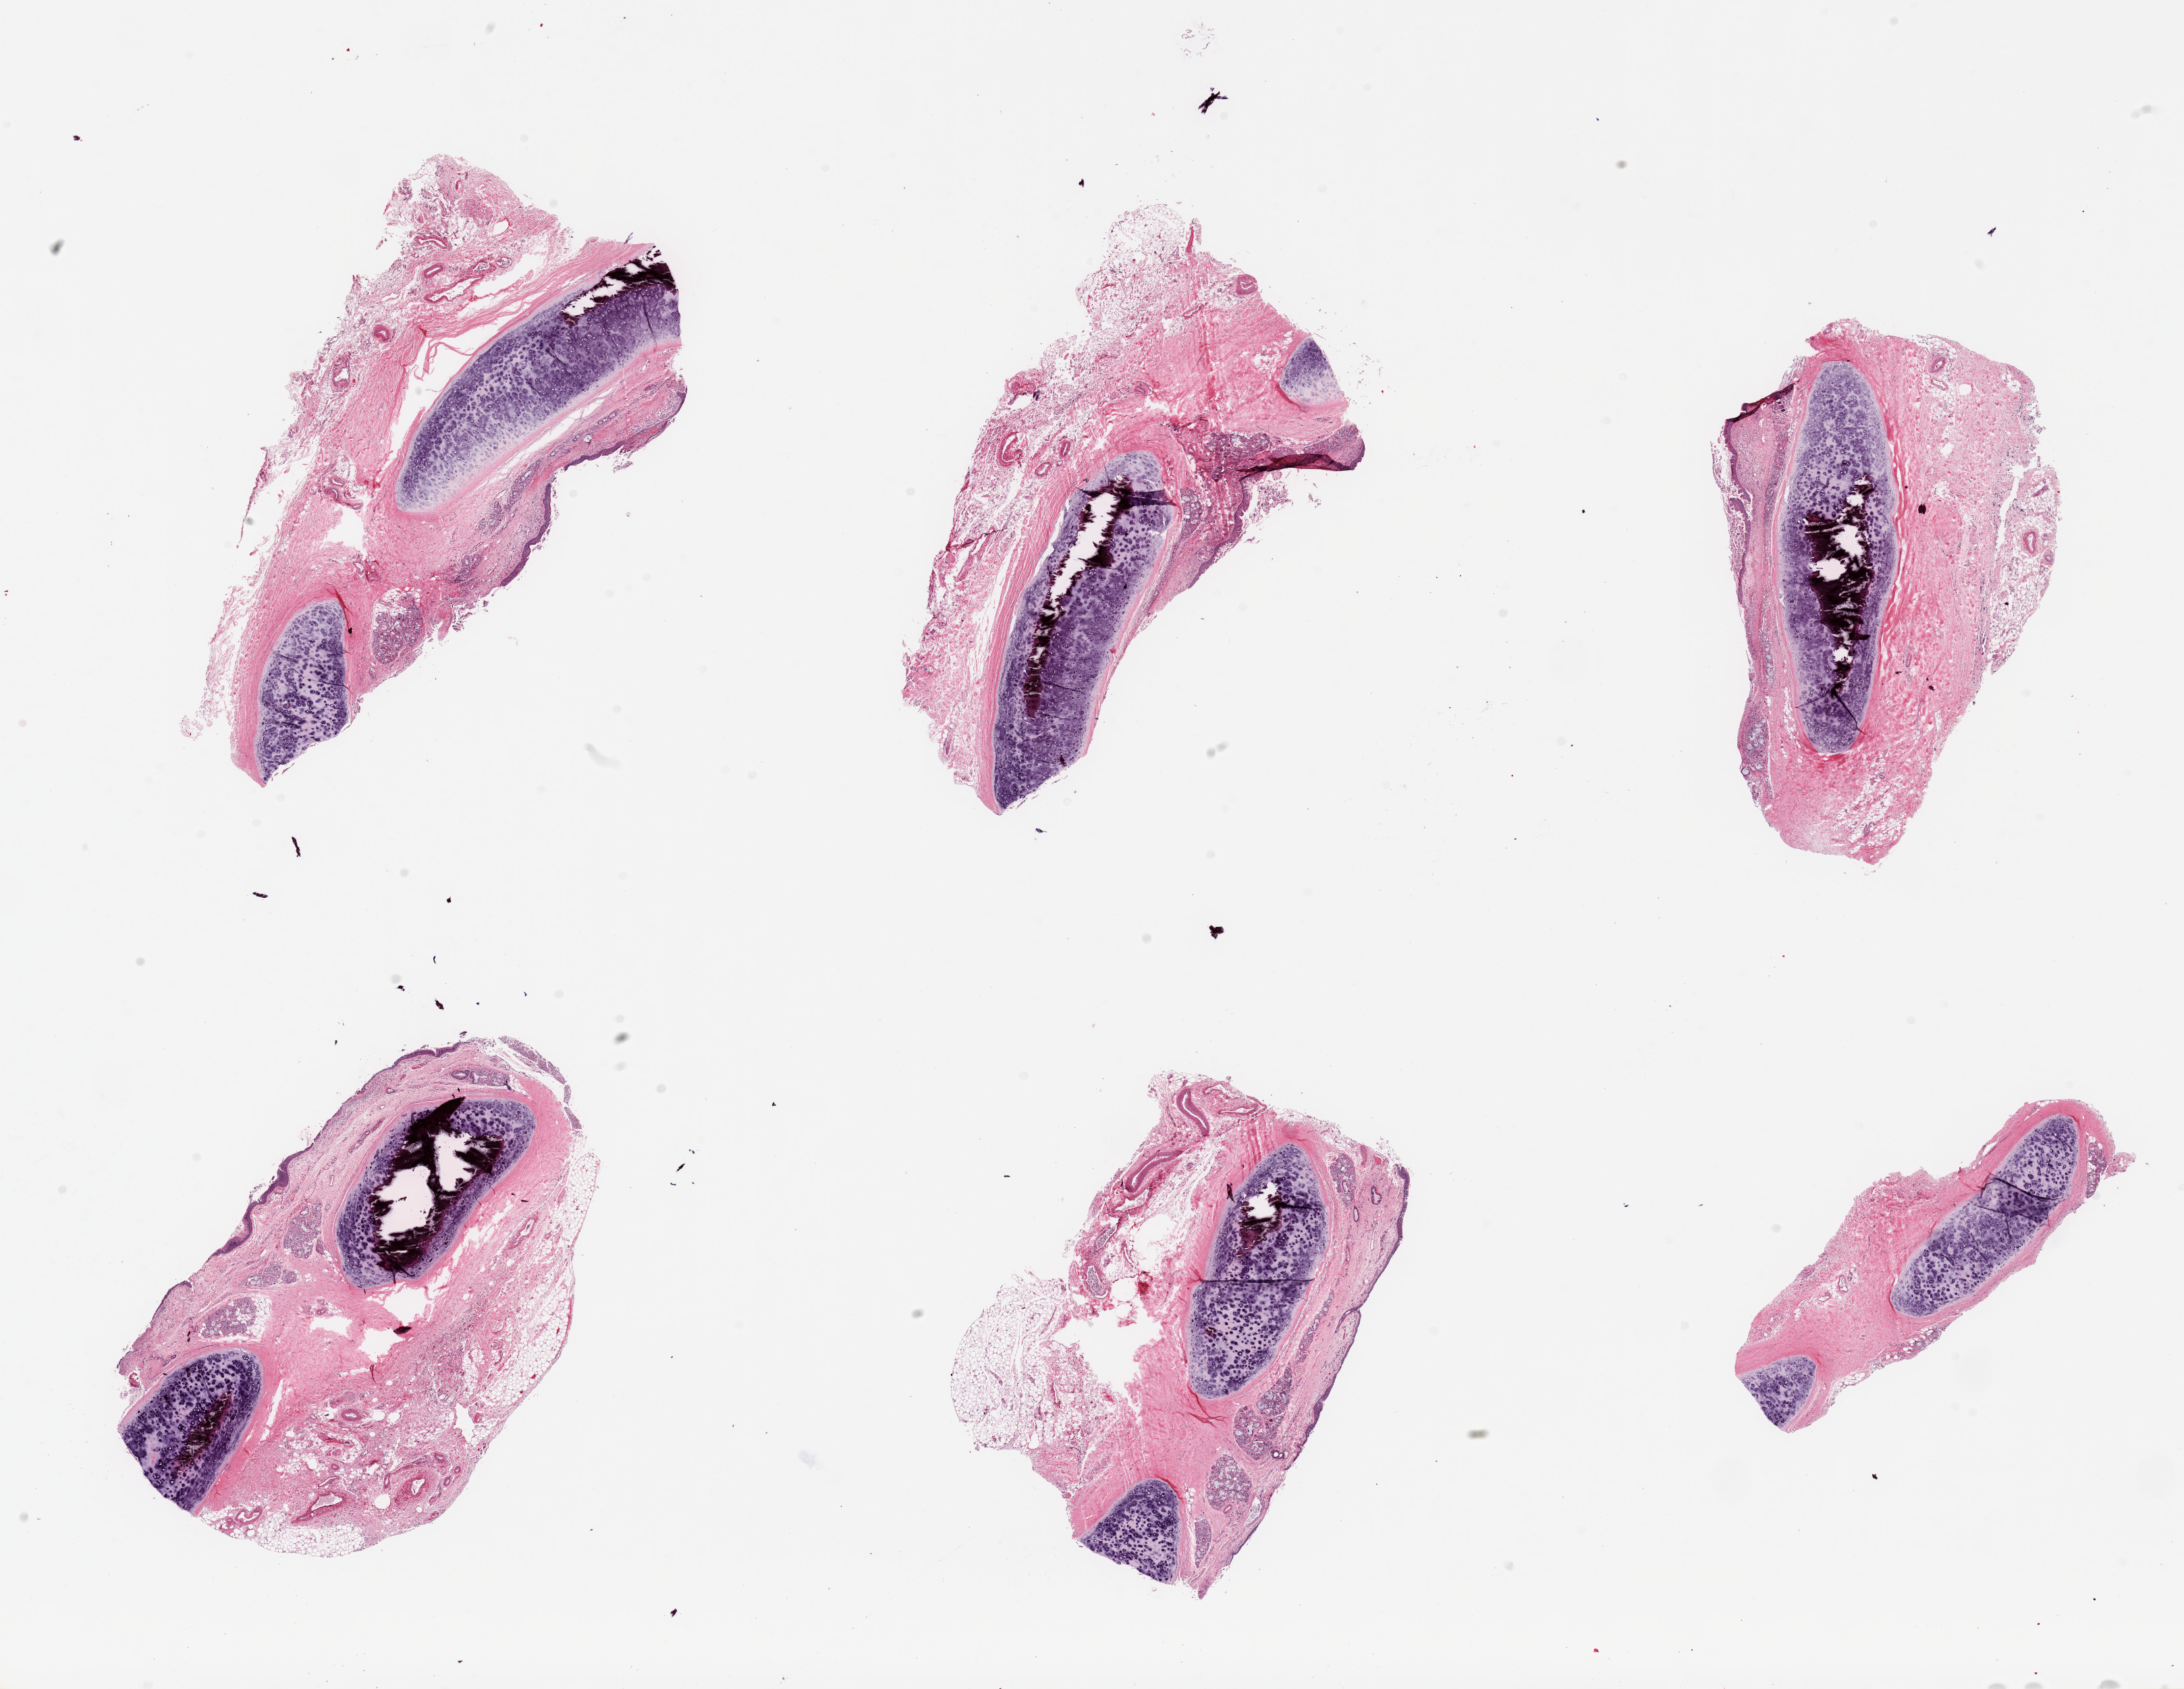
Digitized hematoxylin and eosin (H&E)-stained section, shown as a low-resolution overview of the whole scanned area (about 25.6 x 19.8 mm, slide scanned at 20x), PAXgene-fixed paraffin-embedded (PFPE) section, target tissue: esophageal mucous membrane, tissue donor sample. Female donor.
• review note (as recorded): 6 pieces; trachea sampled